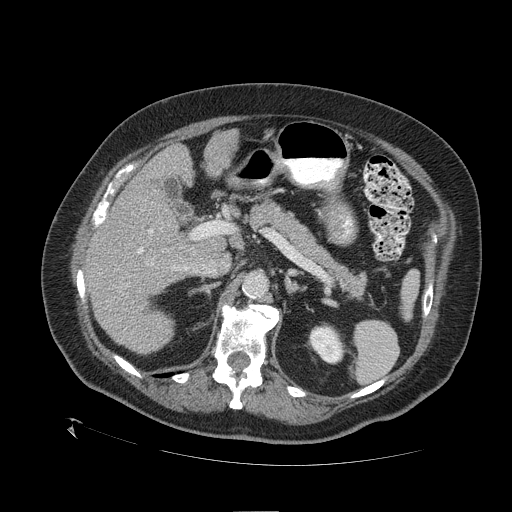
Contrast-enhanced abdominal CT (liver protocol), one axial slice. Slice 65 of 109 in the series (ordered by position). Reconstruction kernel STANDARD. 120 kVp. One of 2 acquisitions stored at this slice position. Soft-tissue window (W 400 / L 40 HU). 2.5 mm slice thickness. 512 × 512 image matrix, field of view 460 × 460 mm. Case-level facts recorded for this patient, not image findings: diagnosis: hepatocellular carcinoma (patient treated with transarterial chemoembolisation; whether this scan precedes or follows treatment is not stated here); TNM stage (as recorded): Stage-I; Child-Pugh class: A; tumour differentiation: no biopsy.
Structures marked on this image (semi-automatic segmentation, software-assisted and operator-edited):
- liver parenchyma outside the tumour (the mass and vessels are separate outlines, so this box may not span the whole liver): bounding box [x1, y1, x2, y2] px = [84, 128, 238, 354]
- liver vessels: [100, 217, 188, 270]